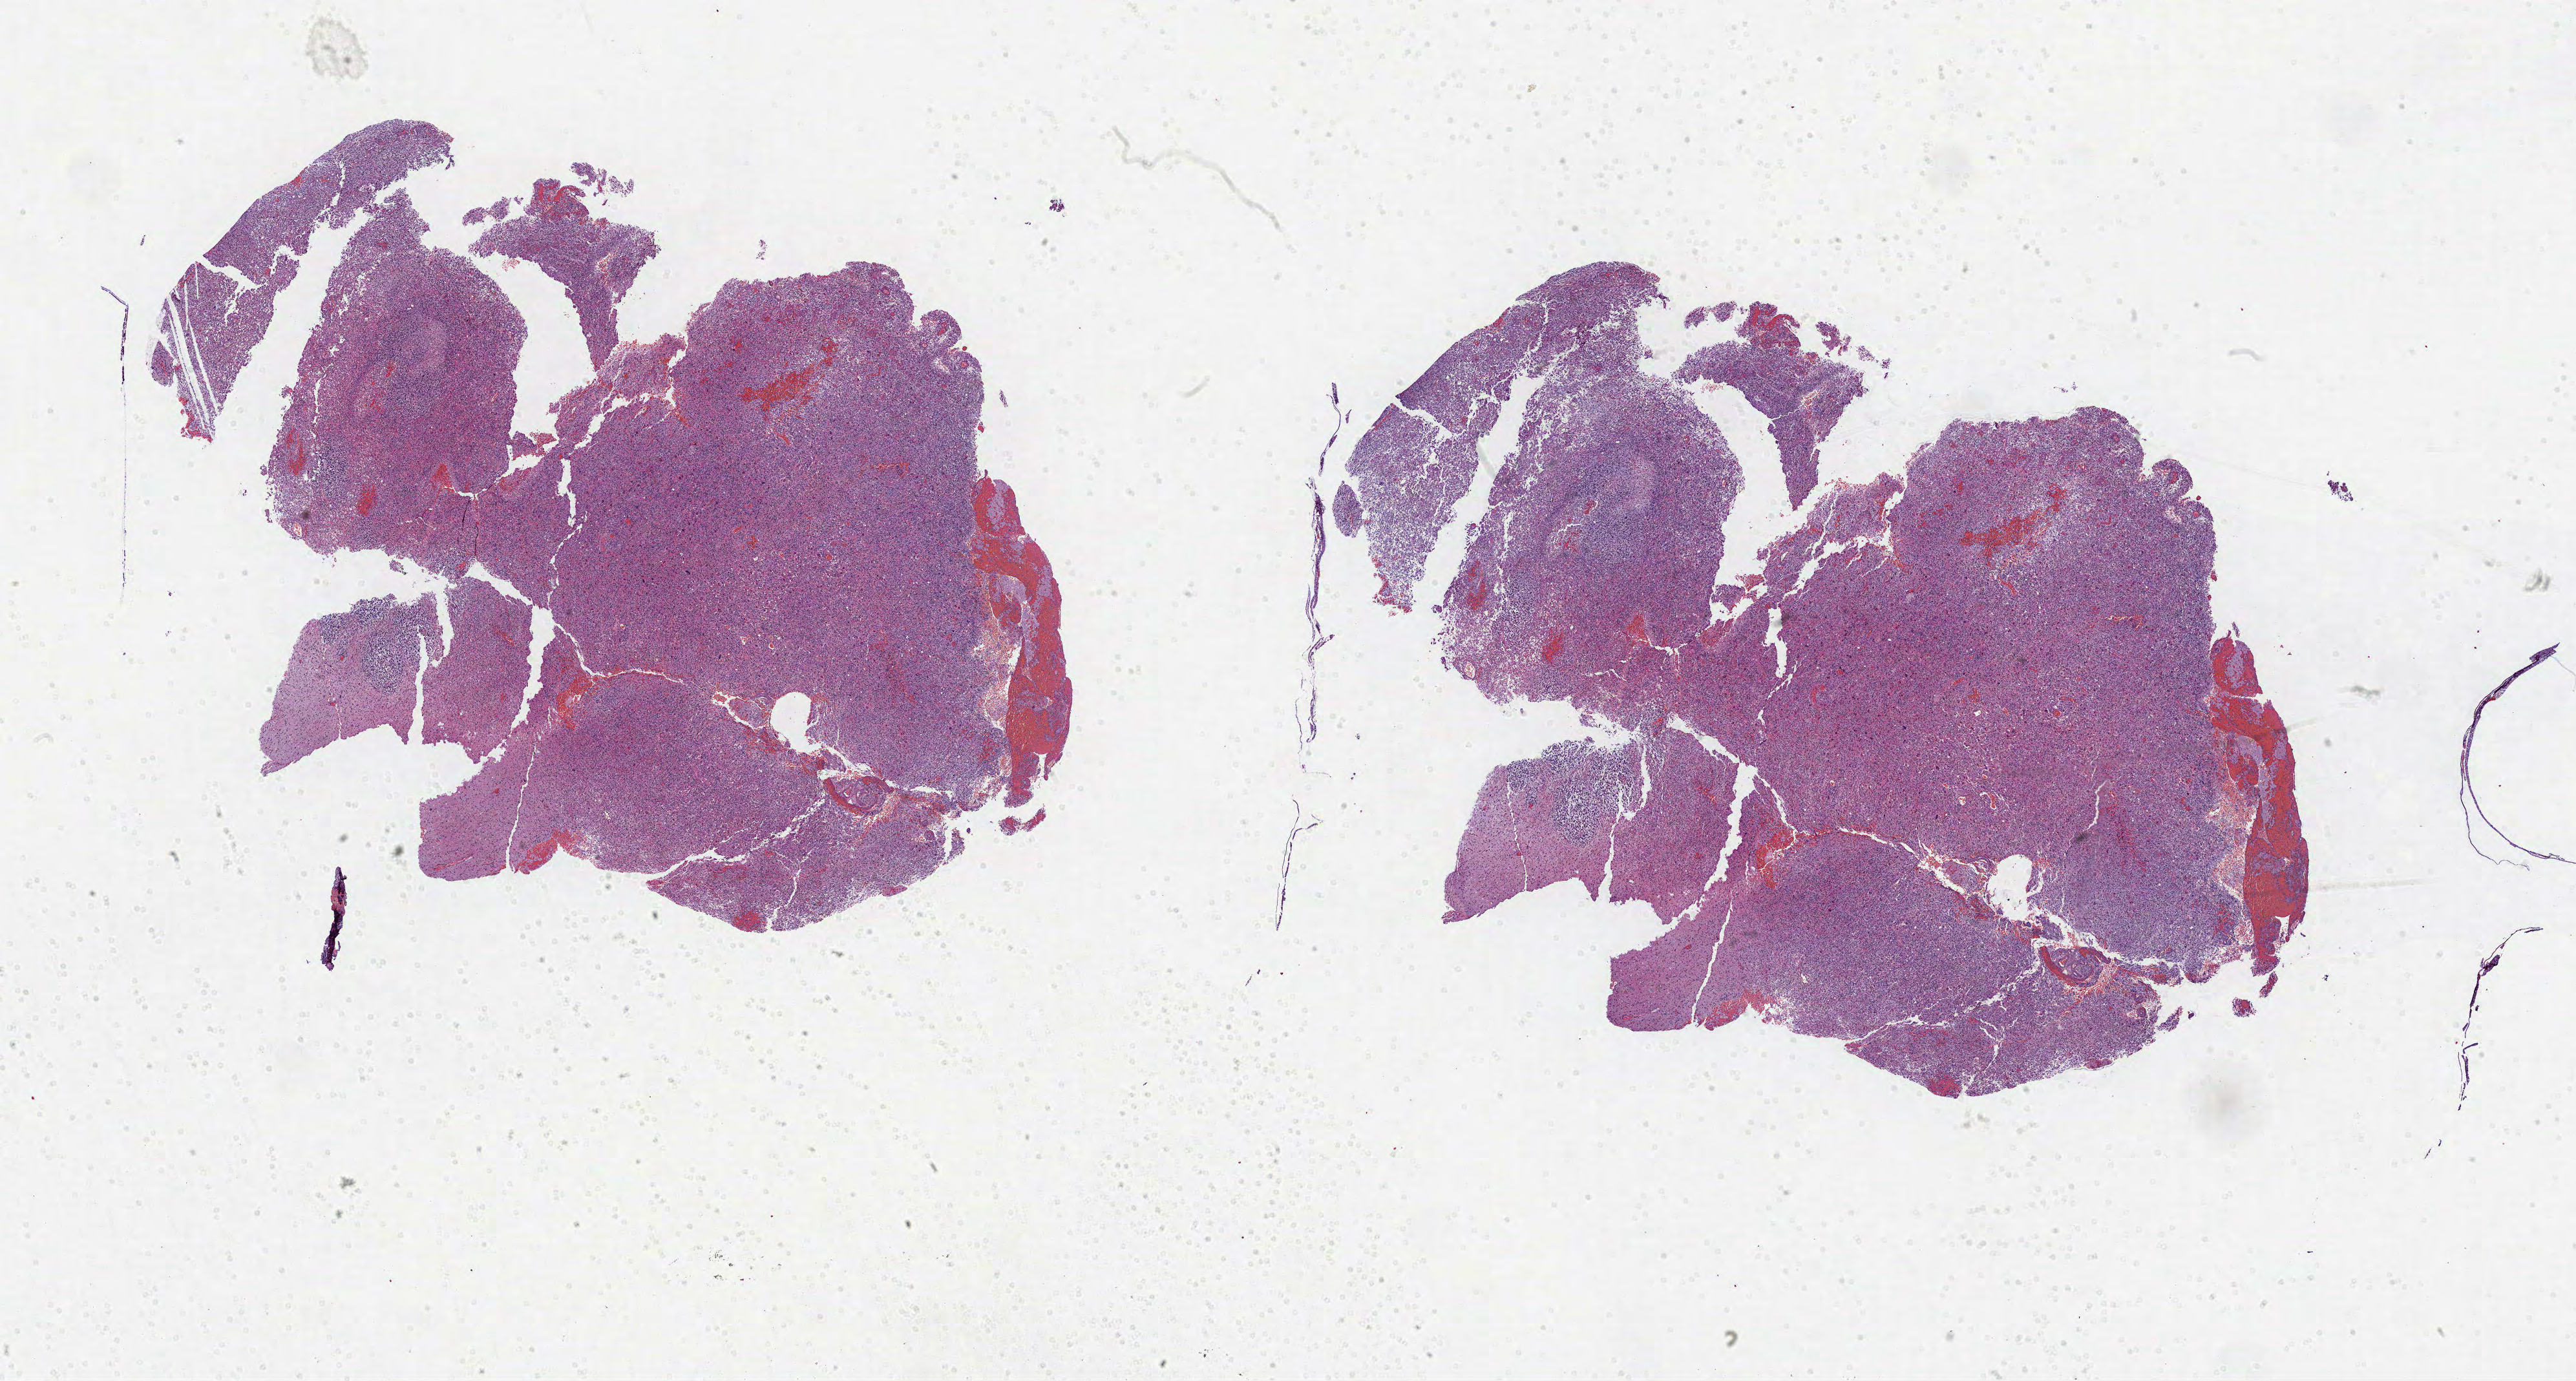
Digitized H&E-stained tissue section (whole slide), shown as a low-resolution overview of the whole scanned area (about 32.1 x 17.2 mm, slide scanned at 40x). Formalin-fixed paraffin-embedded (FFPE) diagnostic section. Sample: primary tumour, brain. Male, age 59 years at initial diagnosis.
• pathologic diagnosis: Glioblastoma